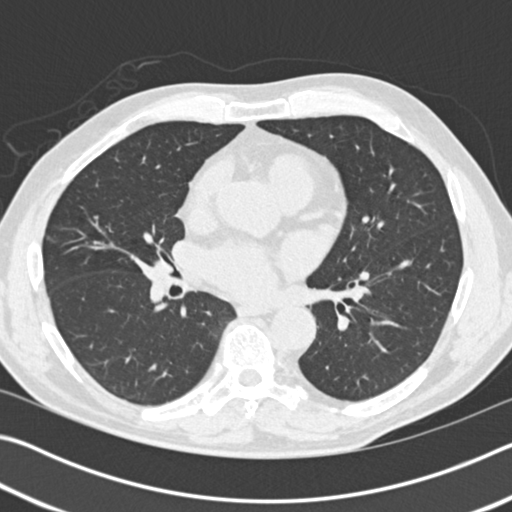
Axial slice from a low-dose chest CT screening exam. First (baseline) screen. Lung window (W 1500 / L -600 HU). 2 mm slice thickness. Male participant, aged 57 years at enrolment.
Expert-annotated lung lesion, bounding box (x1, y1, x2, y2) in pixels: (144, 249, 181, 283). The screening reader recorded 2 non-calcified nodules or masses ≥4 mm on this exam (right middle lobe, right middle lobe); which of them this box marks is not recorded.